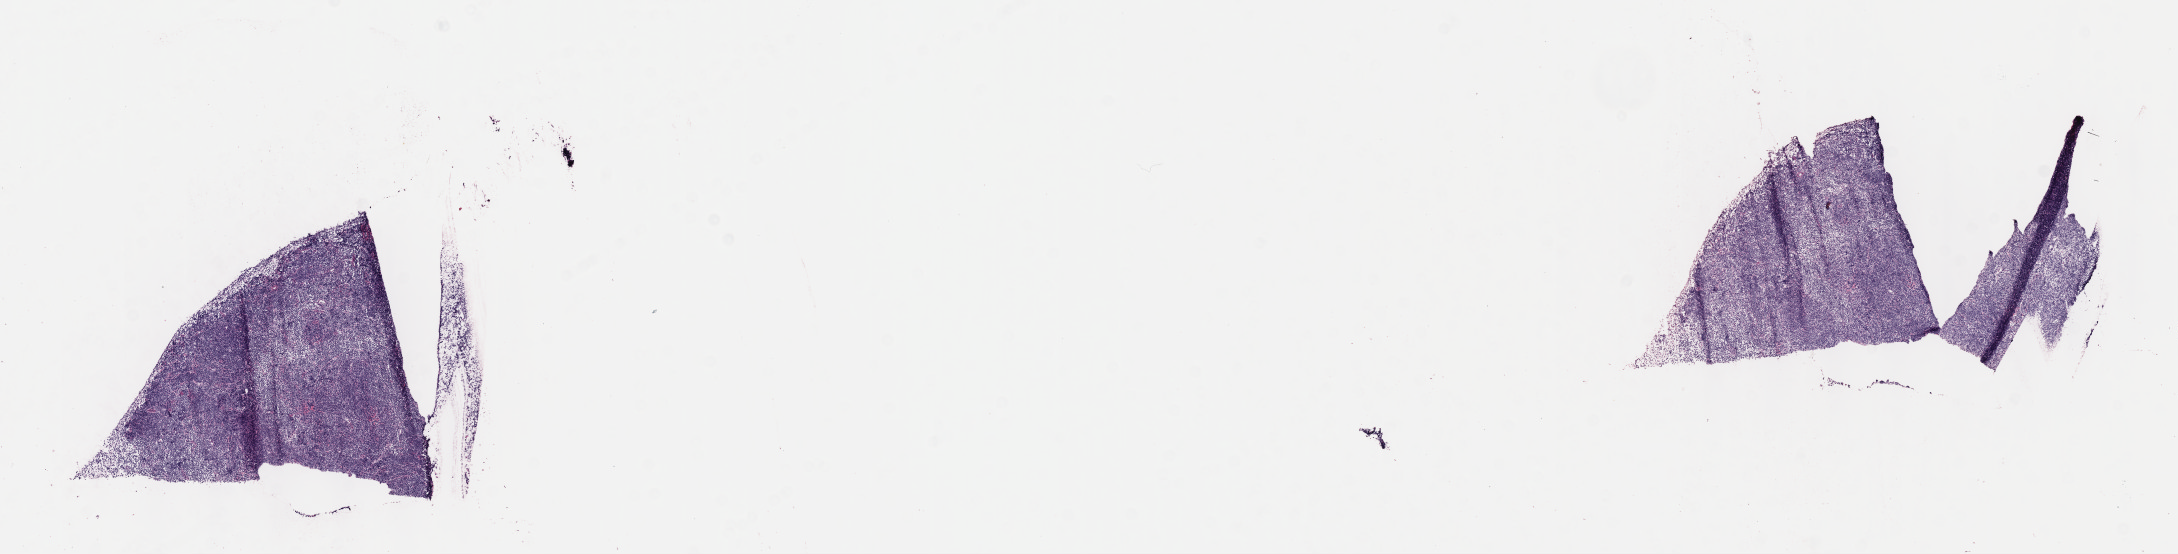
H&E whole-slide image — shown as a low-resolution overview of the whole scanned area (about 17.6 x 4.5 mm). Frozen section (tissue freezing medium). Specimen: primary tumor. Site: cranium. Male patient, aged 12. Slide review estimates, as recorded: tumor cells 90%, tumor nuclei 90%, stromal cells 5%, necrosis 5%, normal cells 0%. Inflammatory infiltration, as recorded: lymphocyte infiltration 5%, monocyte infiltration 10%, neutrophil infiltration 5%.
Diagnosis: Burkitt lymphoma, NOS. Section: bottom of the tissue portion. Ann Arbor stage (patient): Stage I.